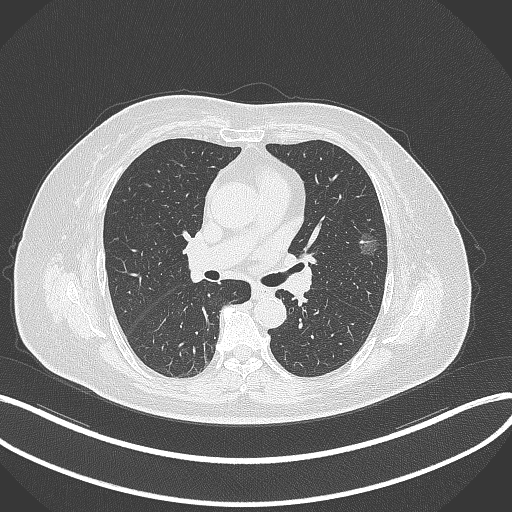
Chest CT, one axial slice. Position 205 of 315 along the scan axis. 120 kVp. Lung window (W 1500 / L -600 HU). 1 mm slice thickness. 512 × 512 image matrix, field of view 400 × 400 mm. Female patient, age 76 years. From the clinical record (not read from this slice): clinical TNM (as recorded): T1b N0 M0; histopathological grade: G1-2.
Outlined on this slice (rectangle marked by the reading radiologist):
- lung tumour (recorded histology: adenocarcinoma): bounding box <354,223,383,260> (left, top, right, bottom; pixels)